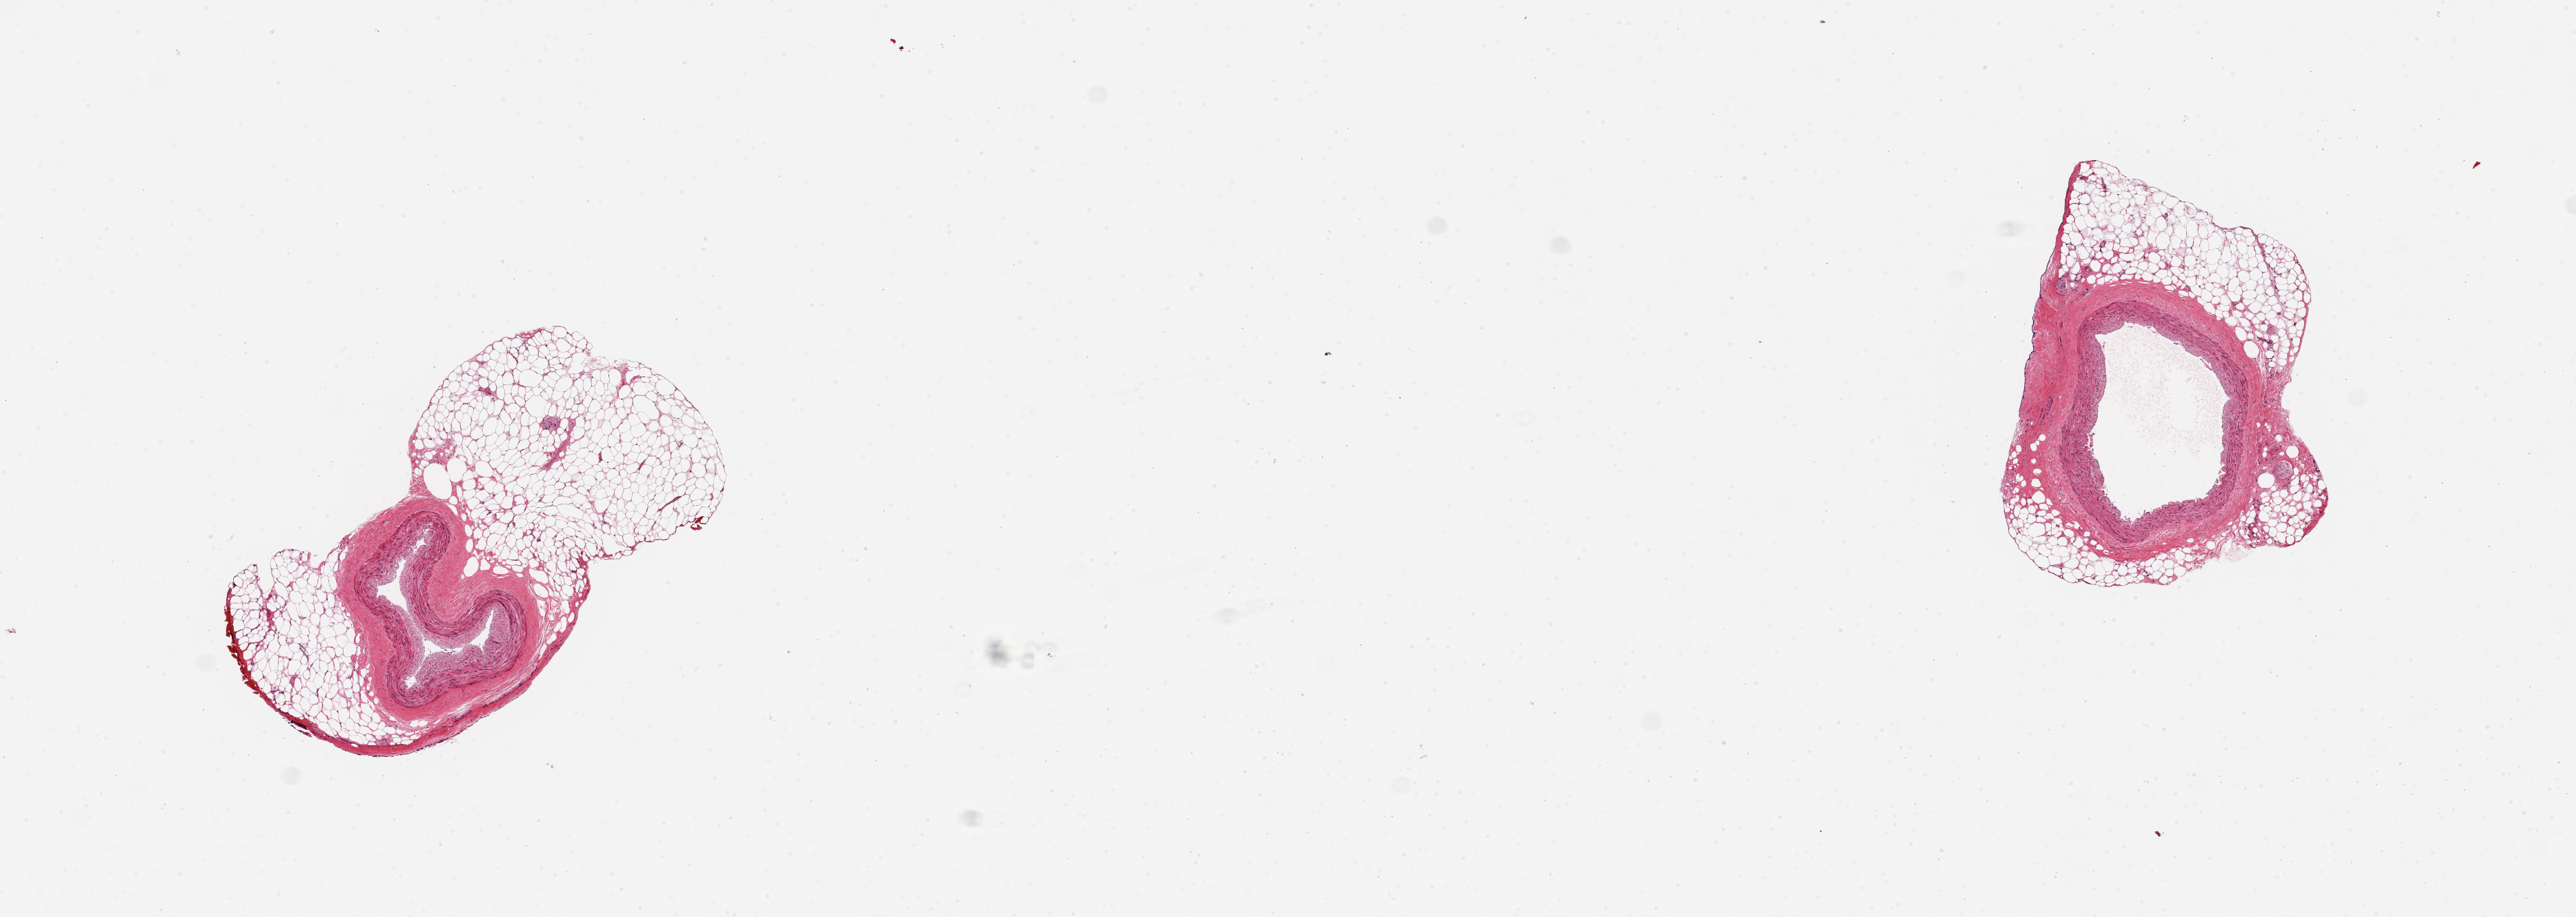
Digitized H&E-stained section, brightfield — low-resolution overview of the scanned area, about 14.8 x 5.3 mm (acquisition: 20x scan), PAXgene-fixed paraffin-embedded (PFPE) section, section of coronary artery (target tissue), tissue donor sample.
Review note (as recorded): 2 pieces; no plaques; up to 1.5 mm external fat , 60%.